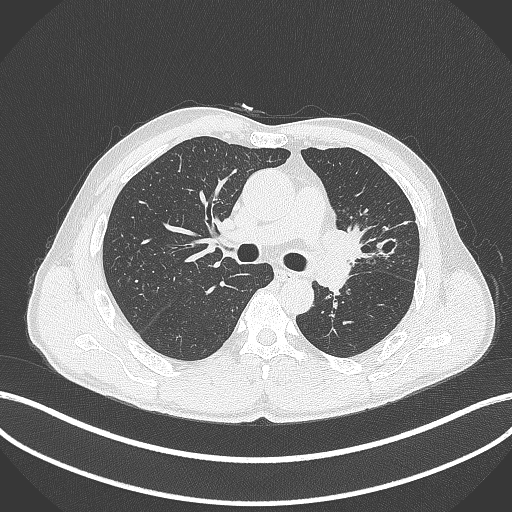
Chest CT, one axial slice; slice 259 of 429 in the series (ordered by position); reconstruction kernel B70f; lung window (W 1500 / L -600 HU); 1 mm slice thickness; 512 × 512 image matrix, field of view 400 × 400 mm. Male patient, age 57 years. From the clinical record (not read from this slice): clinical TNM (as recorded): T2b N0 M0.
Structures marked on this image (bounding box drawn by a radiologist):
- lung tumour (recorded histology: squamous cell carcinoma): bounding box (x1, y1, x2, y2) in pixels: (319, 223, 369, 267)